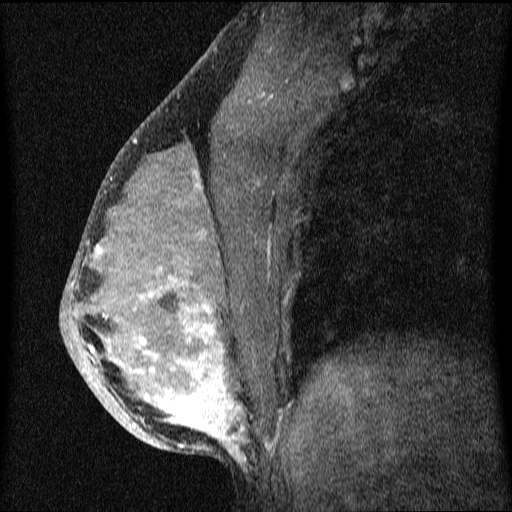
Breast MRI (dynamic contrast-enhanced), one sagittal slice. Slice 33 of 64 in the series (ordered by position). Dynamic contrast-enhanced series, image 2 of 4 at this slice position (ordered by acquisition). 1.5 T. TE 4.2 ms, TR 9.1 ms. 2 mm slice thickness. 512 × 512 image matrix, field of view 180 × 180 mm. Female patient, age 33 years.
Structures marked on this image (semi-automatic segmentation, software-assisted and operator-edited):
- analysis volume of interest (the breast-tissue region the enhancement analysis was run in; not a lesion): bounding box [x1, y1, x2, y2] px = [61, 151, 336, 458]
- tumour enhancement mask (voxels above the 70 % enhancement threshold inside the analysis volume of interest): [90, 174, 246, 458]